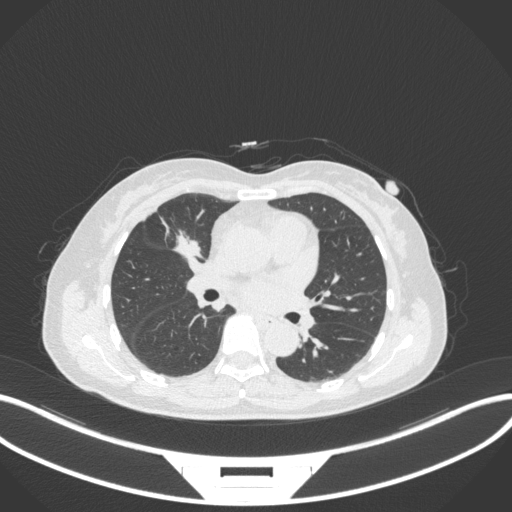
Chest CT, one axial slice. Slice 161 of 282 in the series (ordered by position). 120 kVp. Lung window (W 1500 / L -600 HU). 1 mm slice thickness. 512 × 512 image matrix. Patient: female, 51 years. Case-level facts recorded for this patient, not image findings: clinical TNM (as recorded): T1c N0 M0; histopathological grade: G2.
Annotated regions visible in this slice (bounding box drawn by a radiologist):
- lung tumour (recorded histology: adenocarcinoma): box from (x=169, y=224) to (x=207, y=263) px